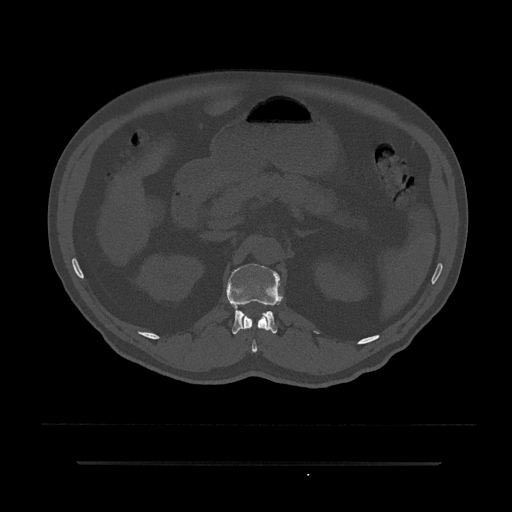
CT including the spine, one axial slice; slice 173 of 797 in the series (ordered by position); bone window (W 1800 / L 400 HU); 0.5 mm slice thickness; 512 × 512 image matrix, field of view 464 × 464 mm. Patient: male, 59 years. From the clinical record (not read from this slice): primary cancer: bile ducts.
Annotated regions visible in this slice (semi-automatically segmented with operator editing):
- L1 vertebra: bounding box (x1, y1, x2, y2) in pixels: (227, 263, 282, 334)
- T12 vertebra: (240, 315, 268, 353)